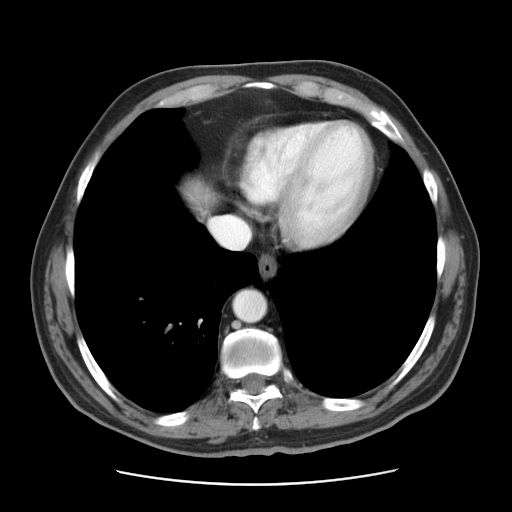
Contrast-enhanced abdominal CT, one axial slice; position 40 of 42 along the scan axis; reconstruction kernel STANDARD; 120 kVp; intravenous contrast given; soft-tissue window (W 400 / L 40 HU); 5 mm slice thickness; 512 × 512 image matrix, field of view 370 × 370 mm. Male patient, age 73 years. Case-level facts recorded for this patient, not image findings: diagnosis: colorectal cancer liver metastases, imaged before liver resection; multiple liver metastases: yes; largest metastasis: 0.5 cm; disease in both lobes: no.
Annotated regions visible in this slice (outlined manually by an expert reader):
- hepatic veins: box from (x=210, y=216) to (x=250, y=248) px